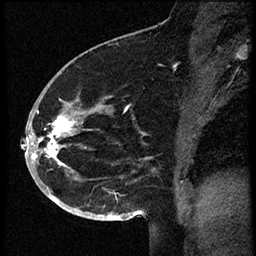
Breast MRI (dynamic contrast-enhanced), one sagittal slice; slice 37 of 60 in the series (ordered by position); dynamic contrast-enhanced study with each time point stored as its own series, time point 2 of 3 at this slice position (early post-contrast, ordered by acquisition time); 1.5 T; TE 4.2 ms, TR 18.9 ms; 256 × 256 image matrix, field of view 200 × 200 mm. Female patient. From the clinical record (not read from this slice): setting: breast cancer imaged before/during neoadjuvant chemotherapy; receptor status: HR-positive, HER2-negative.
Outlined on this slice (semi-automatically segmented with operator editing):
- analysis volume of interest (the breast-tissue region the enhancement analysis was run in; not a lesion): box from (x=30, y=87) to (x=113, y=173) px
- tumour enhancement mask (voxels above the 100 % enhancement threshold inside the analysis volume of interest): (x=31, y=116)–(x=75, y=164)